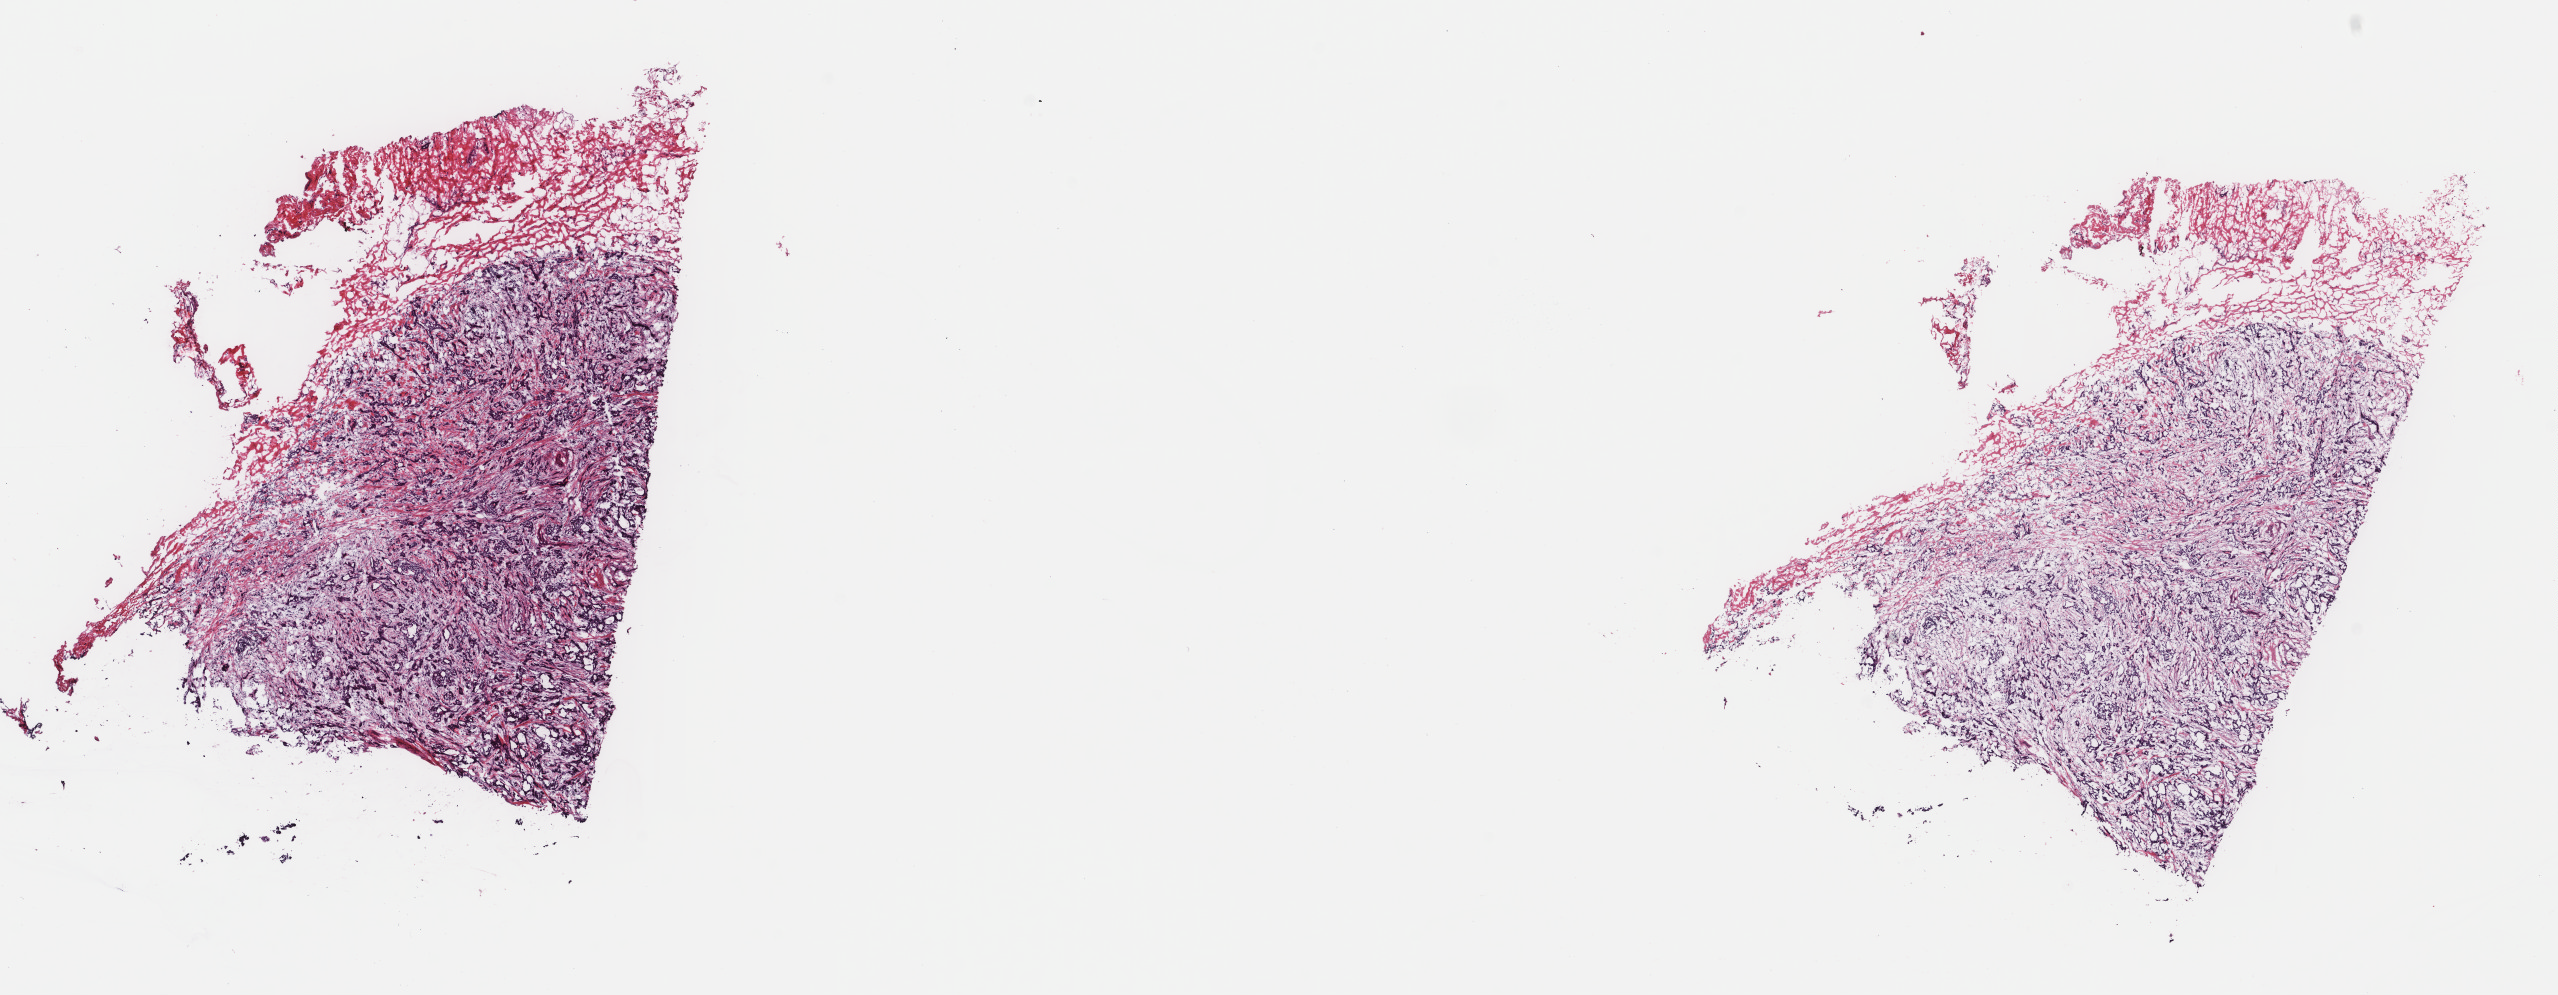
Whole-slide histology image, H&E-stained, shown as a low-resolution overview of the whole scanned area (about 20.3 x 7.9 mm, slide scanned at 40x); frozen section from the top of the tissue portion; breast, primary tumour sample. Patient: female, age at initial diagnosis 50 years. Pathologist review of this section (percent, as recorded): tumour cells 70%, tumour nuclei 82%, normal cells 0%, stromal cells 30%, necrosis 0%. Infiltration values recorded for this section: lymphocyte infiltration 1%, monocyte infiltration 0%, neutrophil infiltration 0%.
Histologic diagnosis: Infiltrating duct carcinoma, NOS. Lymph nodes positive (case pathology): 3 of 14 examined. Laterality: left. TNM: T2 N1a M0. AJCC pathologic stage: IIB (7th edition).